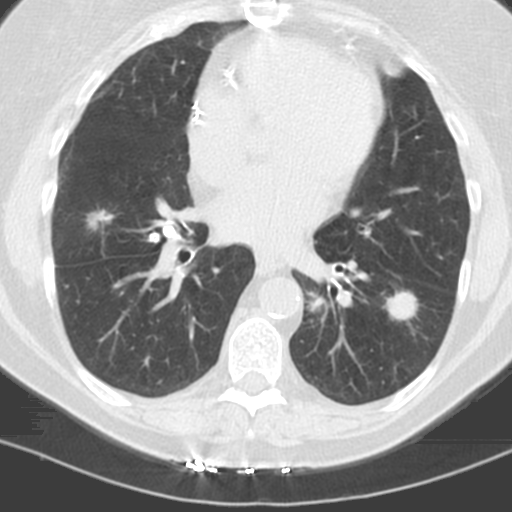
Low-dose screening chest CT, one axial slice. 120 kVp. Lung window (W 1500 / L -600 HU). 512 × 512 image matrix, field of view 278 × 278 mm.
Outlined on this slice (manually delineated by an expert):
- lesion 1 (tumor, lower lobe of left lung): box from (x=387, y=291) to (x=418, y=321) px
- lesion 3 (tumor, middle lobe of right lung): (x=88, y=211)–(x=111, y=229)